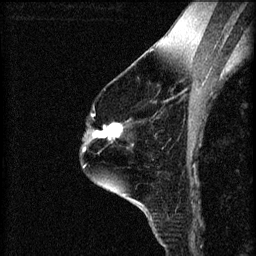
Breast MRI (dynamic contrast-enhanced), one sagittal slice. Position 43 of 60 along the scan axis. 3 images stored at this slice position (order not interpretable as contrast timing). 1.5 T. TE 4.2 ms, TR 8.2 ms. 256 × 256 image matrix. Patient: female, 60 years.
Structures marked on this image (semi-automatically segmented with operator editing):
- analysis volume of interest (the breast-tissue region the enhancement analysis was run in; not a lesion): box from (x=89, y=116) to (x=123, y=143) px
- tumour enhancement mask (voxels above the 70 % enhancement threshold inside the analysis volume of interest): (x=92, y=116)–(x=123, y=141)